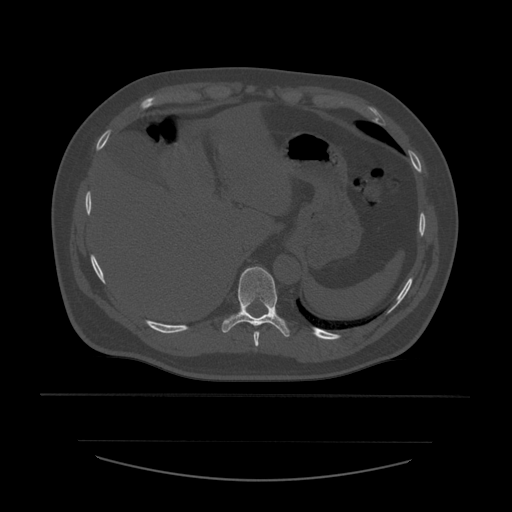
CT including the spine, one axial slice; slice 299 of 532 in the series (ordered by position); bone window (W 1800 / L 400 HU); 512 × 512 image matrix. Patient age 44 years. From the clinical record (not read from this slice): primary cancer: soft tissue sarcoma.
Structures marked on this image (semi-automatically segmented with operator editing):
- T10 vertebra: bounding box <222,267,290,337> (left, top, right, bottom; pixels)
- T9 vertebra: <254,331,260,347>